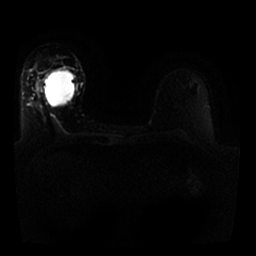
Breast MRI, one axial slice. Slice 13 of 25 in the series (ordered by position). Diffusion-weighted series; image 2 of 4 stored at this slice position (different b-values; order by instance number). 1.5 T. 4 mm slice thickness. 256 × 256 image matrix. Female patient.
Annotated regions visible in this slice (manually delineated by an expert):
- tumour on diffusion-weighted imaging: box from (x=44, y=68) to (x=67, y=80) px